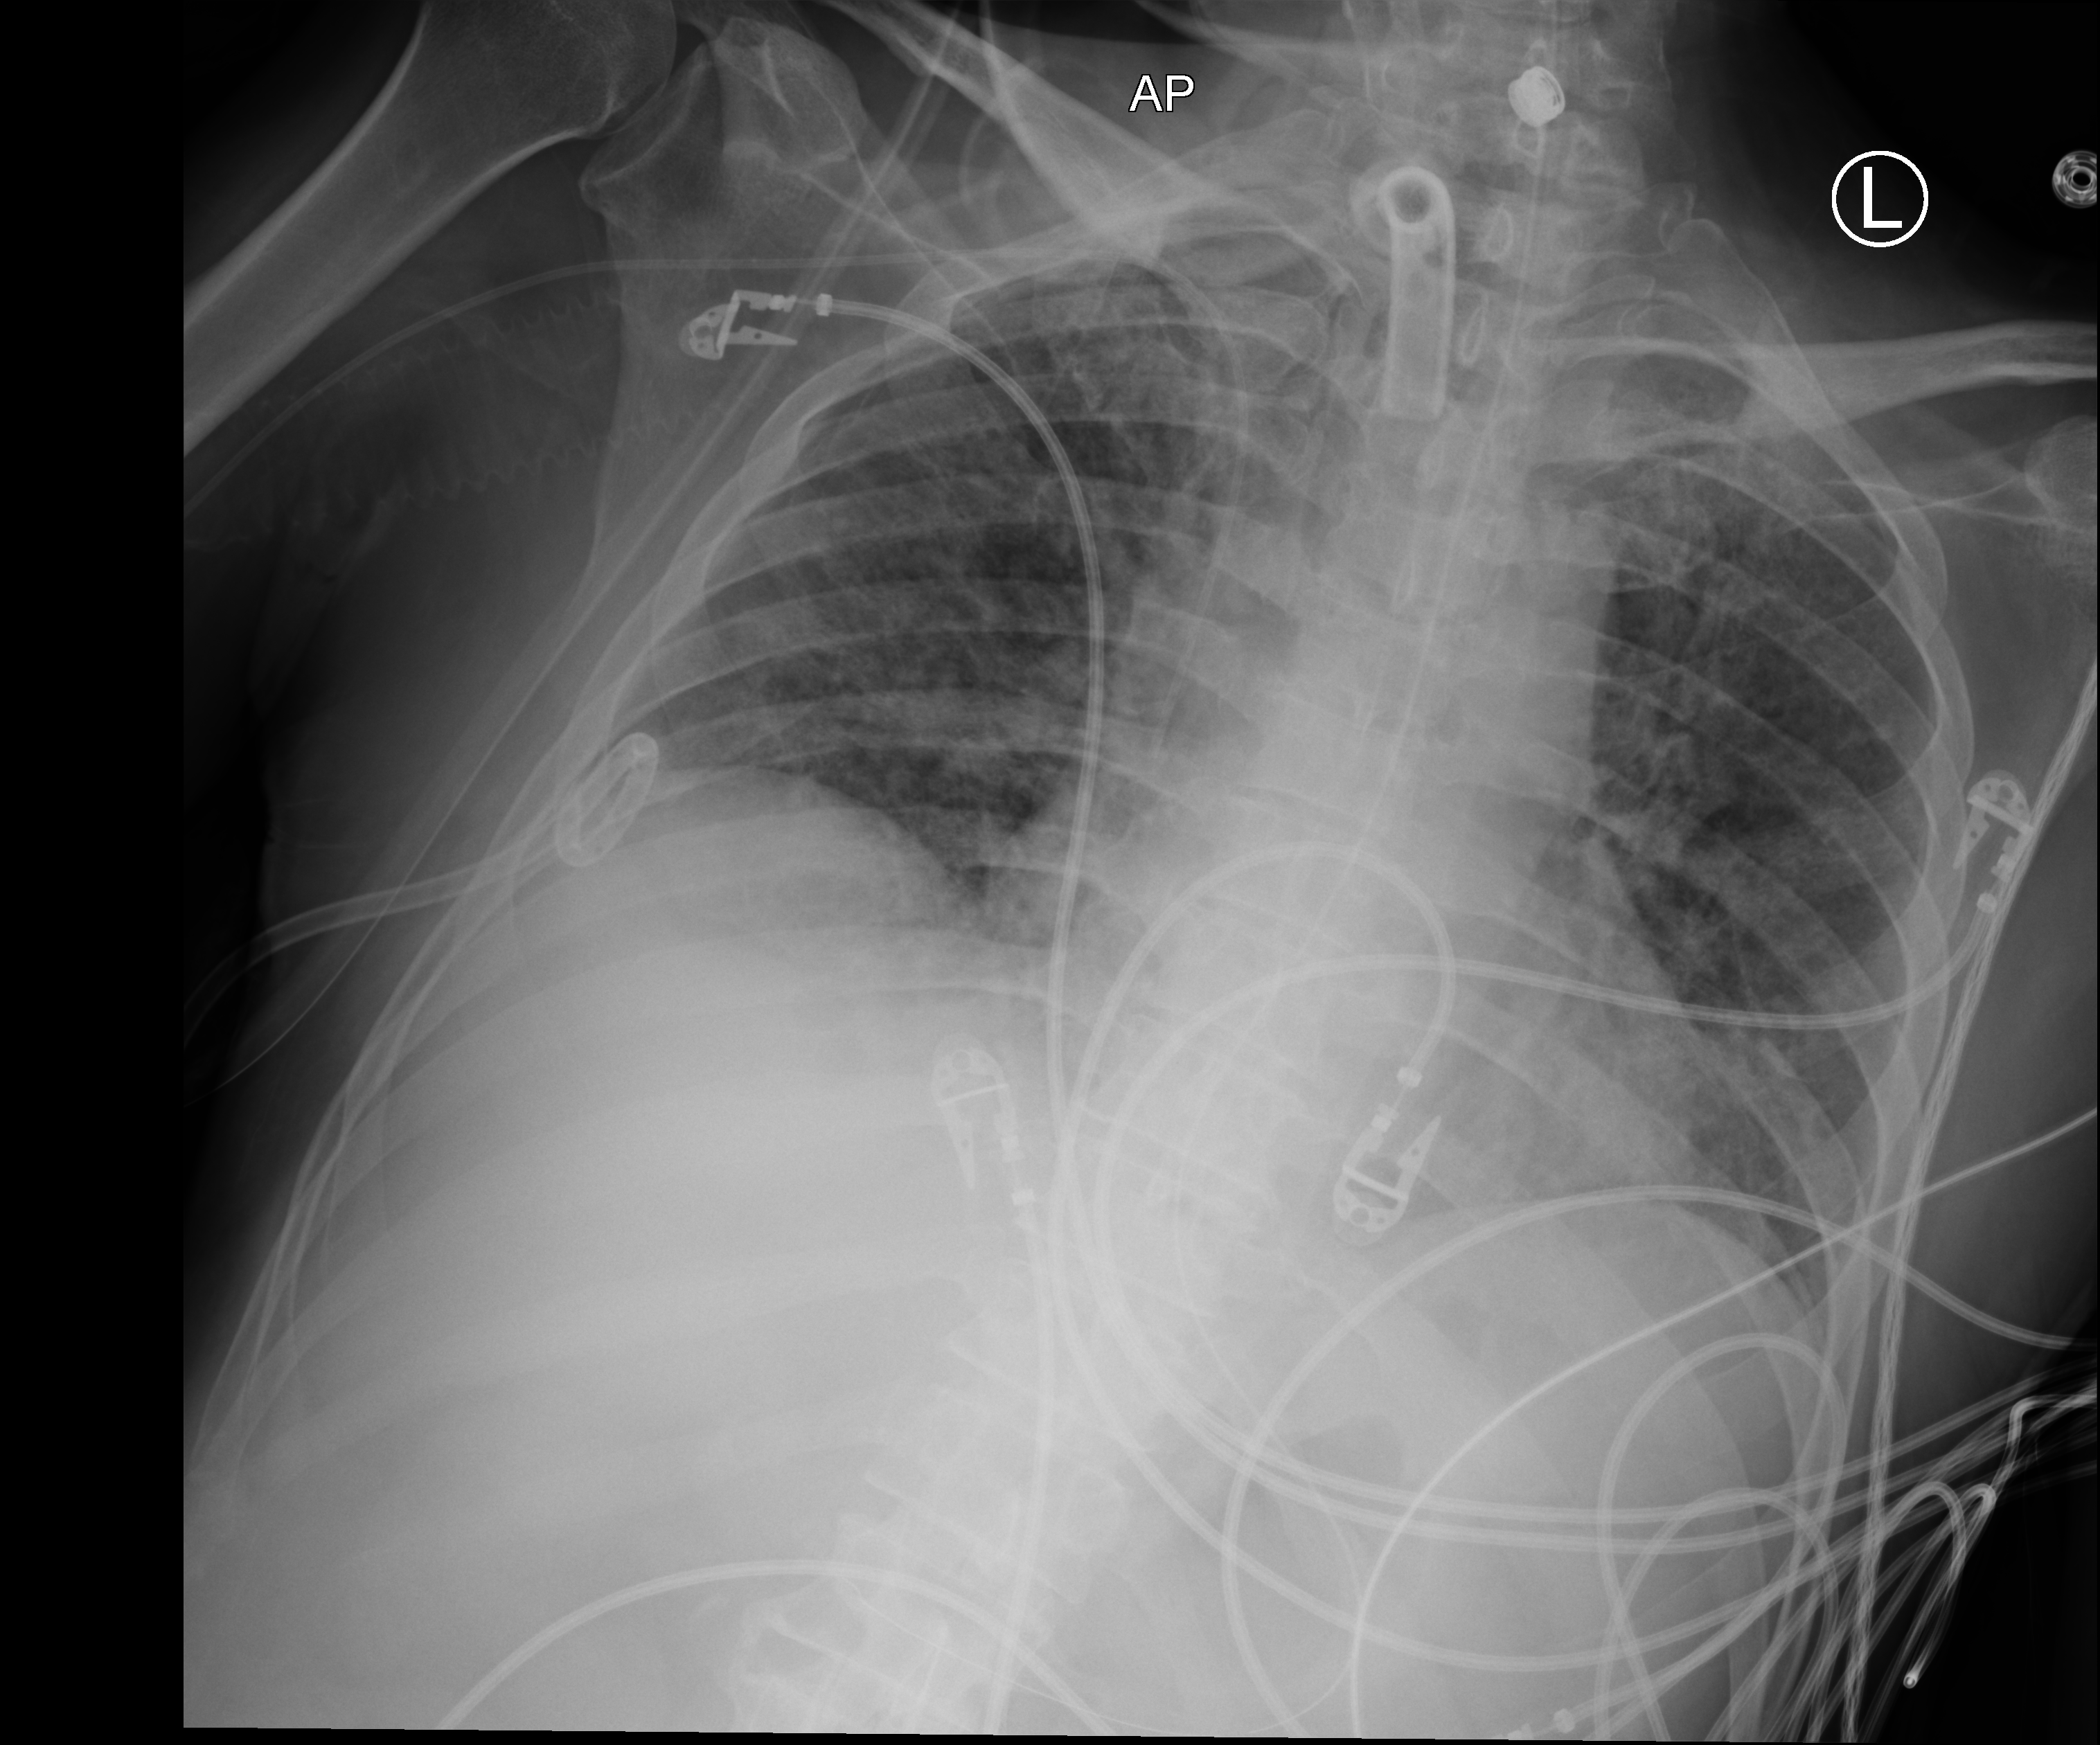
Bedside chest radiograph (computed radiography), anteroposterior (AP) projection. Male patient hospitalised with COVID-19, age 18–59 years.
Admission-level facts for this patient (not findings on this image; timing relative to this image not recorded):
- diabetes (admission record): no